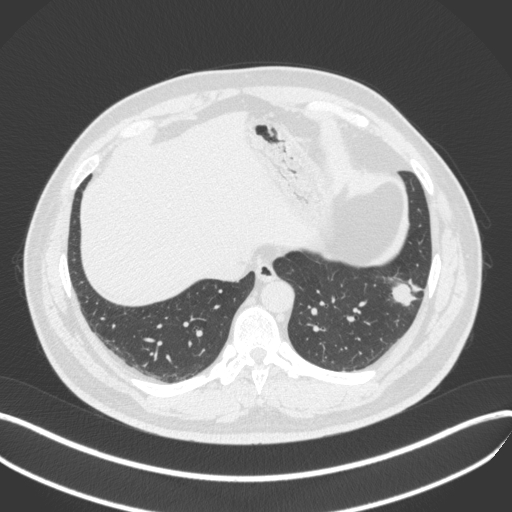
Chest CT, one axial slice. Position 113 of 420 along the scan axis. Reconstruction kernel B31f. Lung window (W 1500 / L -600 HU). 1 mm slice thickness. 512 × 512 image matrix, field of view 400 × 400 mm. Male patient, age 39 years. From the clinical record (not read from this slice): clinical TNM (as recorded): T2a N0 M0.
Structures marked on this image (bounding box drawn by a radiologist):
- lung tumour (recorded histology: adenocarcinoma): box from (x=387, y=272) to (x=425, y=311) px